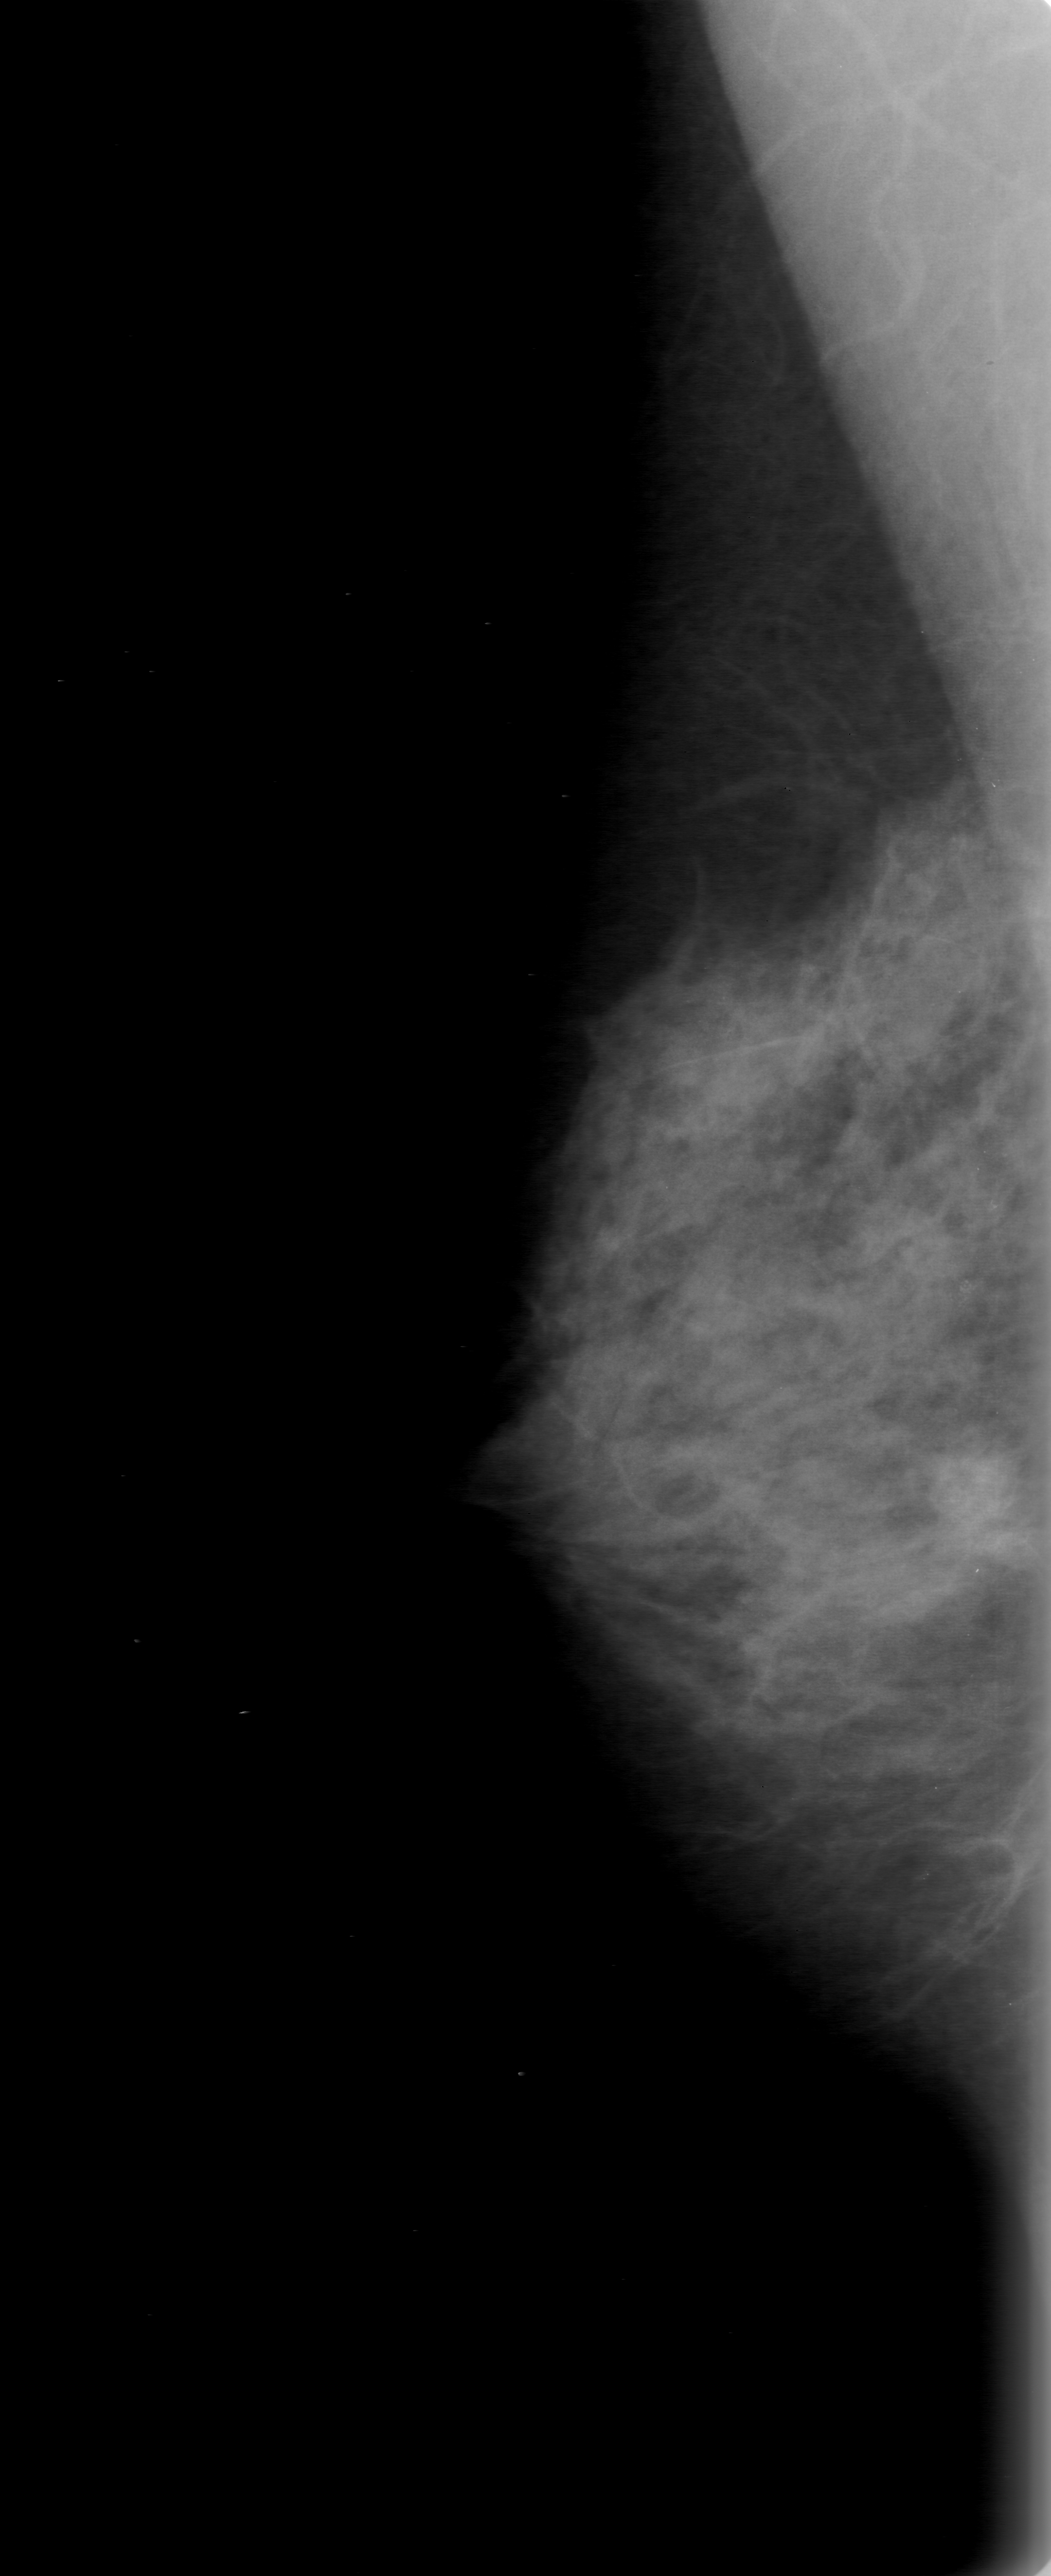
Digitized screen-film mammogram; right breast; mediolateral oblique (MLO) view; breast composition: heterogeneously dense (BI-RADS density category 3 of 4); 1051 × 2576 image matrix.
Marked abnormalities (boxes around the expert regions of interest):
- mass, shape irregular, margins ill defined; BI-RADS assessment category 0 (incomplete: needs additional imaging); pathology result (as recorded, not read from the image): malignant: box from (x=881, y=1423) to (x=1020, y=1562) px